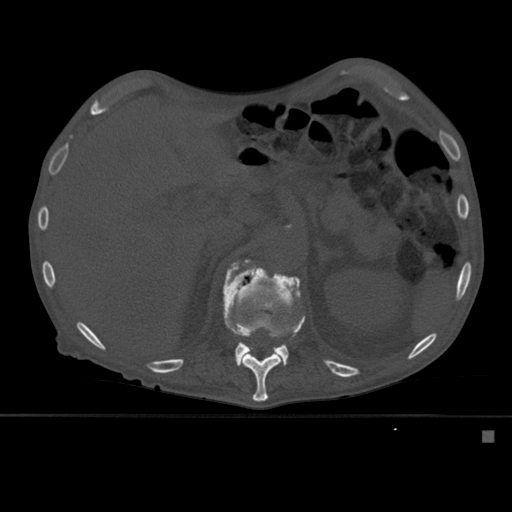
CT including the spine, one axial slice; position 269 of 527 along the scan axis; bone window (W 1800 / L 400 HU); 1.5 mm slice thickness; 512 × 512 image matrix. Patient: male, 78 years. Case-level facts recorded for this patient, not image findings: primary cancer: prostate.
Structures marked on this image (semi-automatically segmented with operator editing):
- L1 vertebra: bounding box (x1, y1, x2, y2) in pixels: (223, 265, 300, 402)
- T12 vertebra: (223, 259, 305, 401)